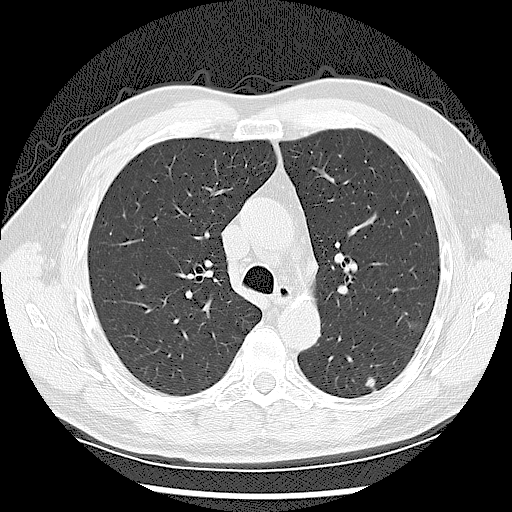
Low-dose screening chest CT, axial slice, baseline annual screen, lung window (W 1500 / L -600 HU), 2.5 mm slice thickness. Male, age 65 years at enrolment. Former smoker at enrolment.
Expert-annotated lung lesion, bounding box [x1, y1, x2, y2] px = [355, 368, 391, 402]. The exam's reader record, not a measurement of the box and not confirmed to be the same lesion: non-calcified nodule or mass ≥4 mm, left lower lobe, 7 × 7 mm, smooth margins, soft tissue attenuation. Later outcome: lung cancer diagnosed 375 days after this screen (after the second annual screen) — adenocarcinoma, NOS, left lower lobe, well differentiated (G1), stage IB (AJCC 6th edition), 10 mm at pathology.